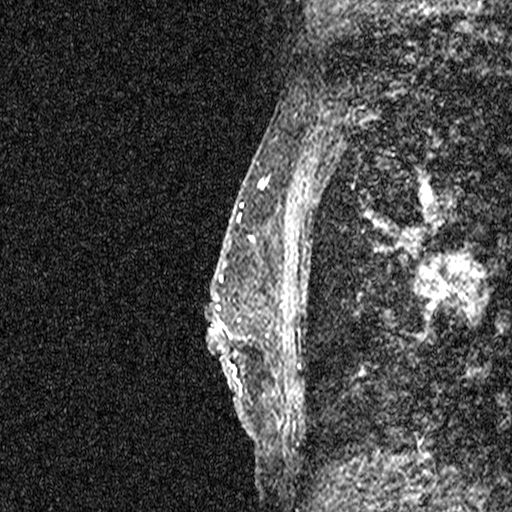
Breast MRI (dynamic contrast-enhanced), one sagittal slice; position 20 of 44 along the scan axis; dynamic contrast-enhanced study with each time point stored as its own series, time point 2 of 3 at this slice position (early post-contrast, ordered by acquisition time); 1.5 T; TE 4.5 ms, TR 11 ms; 2.05 mm slice thickness; 512 × 512 image matrix, field of view 200 × 200 mm. Female patient, age 44 years. Case-level facts recorded for this patient, not image findings: setting: breast cancer imaged before/during neoadjuvant chemotherapy; receptor status: HR-positive, HER2-negative.
Outlined on this slice (semi-automatically segmented with operator editing):
- analysis volume of interest (the breast-tissue region the enhancement analysis was run in; not a lesion): bounding box (x1, y1, x2, y2) in pixels: (204, 254, 273, 401)
- tumour enhancement mask (voxels above the 90 % enhancement threshold inside the analysis volume of interest): (209, 258, 269, 394)